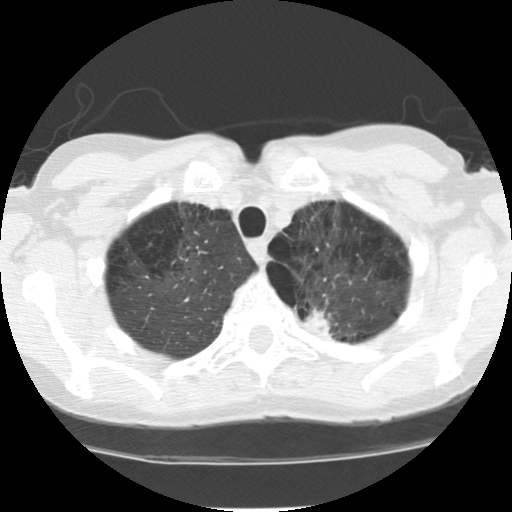
Low-dose screening chest CT, one axial slice. Position 99 of 116 along the scan axis. Reconstruction kernel STANDARD. 120 kVp. Lung window (W 1500 / L -600 HU). 512 × 512 image matrix, field of view 300 × 300 mm.
Structures marked on this image (outlined manually by an expert reader):
- lesion 1 (tumor, upper lobe of left lung): box from (x=302, y=308) to (x=333, y=338) px